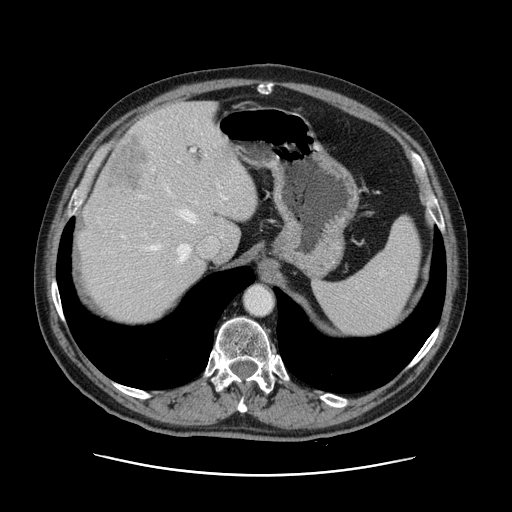
Contrast-enhanced abdominal CT, one axial slice. Position 96 of 141 along the scan axis. 120 kVp. Intravenous contrast given. Soft-tissue window (W 400 / L 40 HU). 2.5 mm slice thickness. 512 × 512 image matrix. Male patient, age 72 years. From the clinical record (not read from this slice): diagnosis: colorectal cancer liver metastases, imaged before liver resection; multiple liver metastases: yes; largest metastasis: 5.4 cm; disease in both lobes: yes.
Structures marked on this image (outlined manually by an expert reader):
- hepatic veins: bounding box (x1, y1, x2, y2) in pixels: (123, 187, 196, 262)
- liver: (76, 102, 258, 326)
- planned liver remnant (the part of the liver to remain after resection): (78, 102, 258, 326)
- portal vein (with intrahepatic branches): (181, 149, 225, 255)
- liver metastasis: (104, 132, 151, 192)